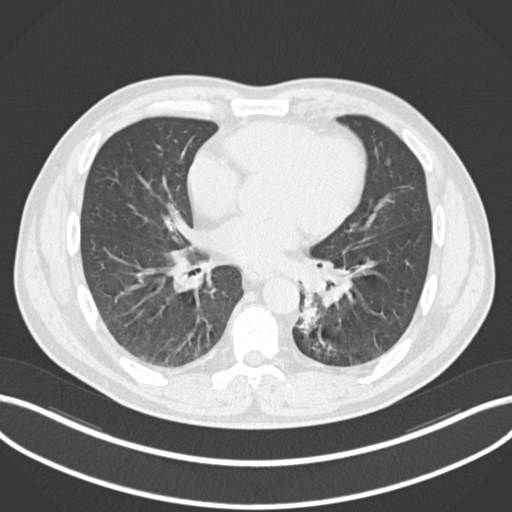
Chest CT, one axial slice; position 98 of 223 along the scan axis; reconstruction kernel B30f; lung window (W 1500 / L -600 HU); 1 mm slice thickness; 512 × 512 image matrix, field of view 400 × 400 mm. Patient: male, 50 years. From the clinical record (not read from this slice): clinical TNM (as recorded): T2a N3 M0.
Annotated regions visible in this slice (rectangle marked by the reading radiologist):
- lung tumour (recorded histology: squamous cell carcinoma): bounding box (x1, y1, x2, y2) in pixels: (295, 292, 322, 332)